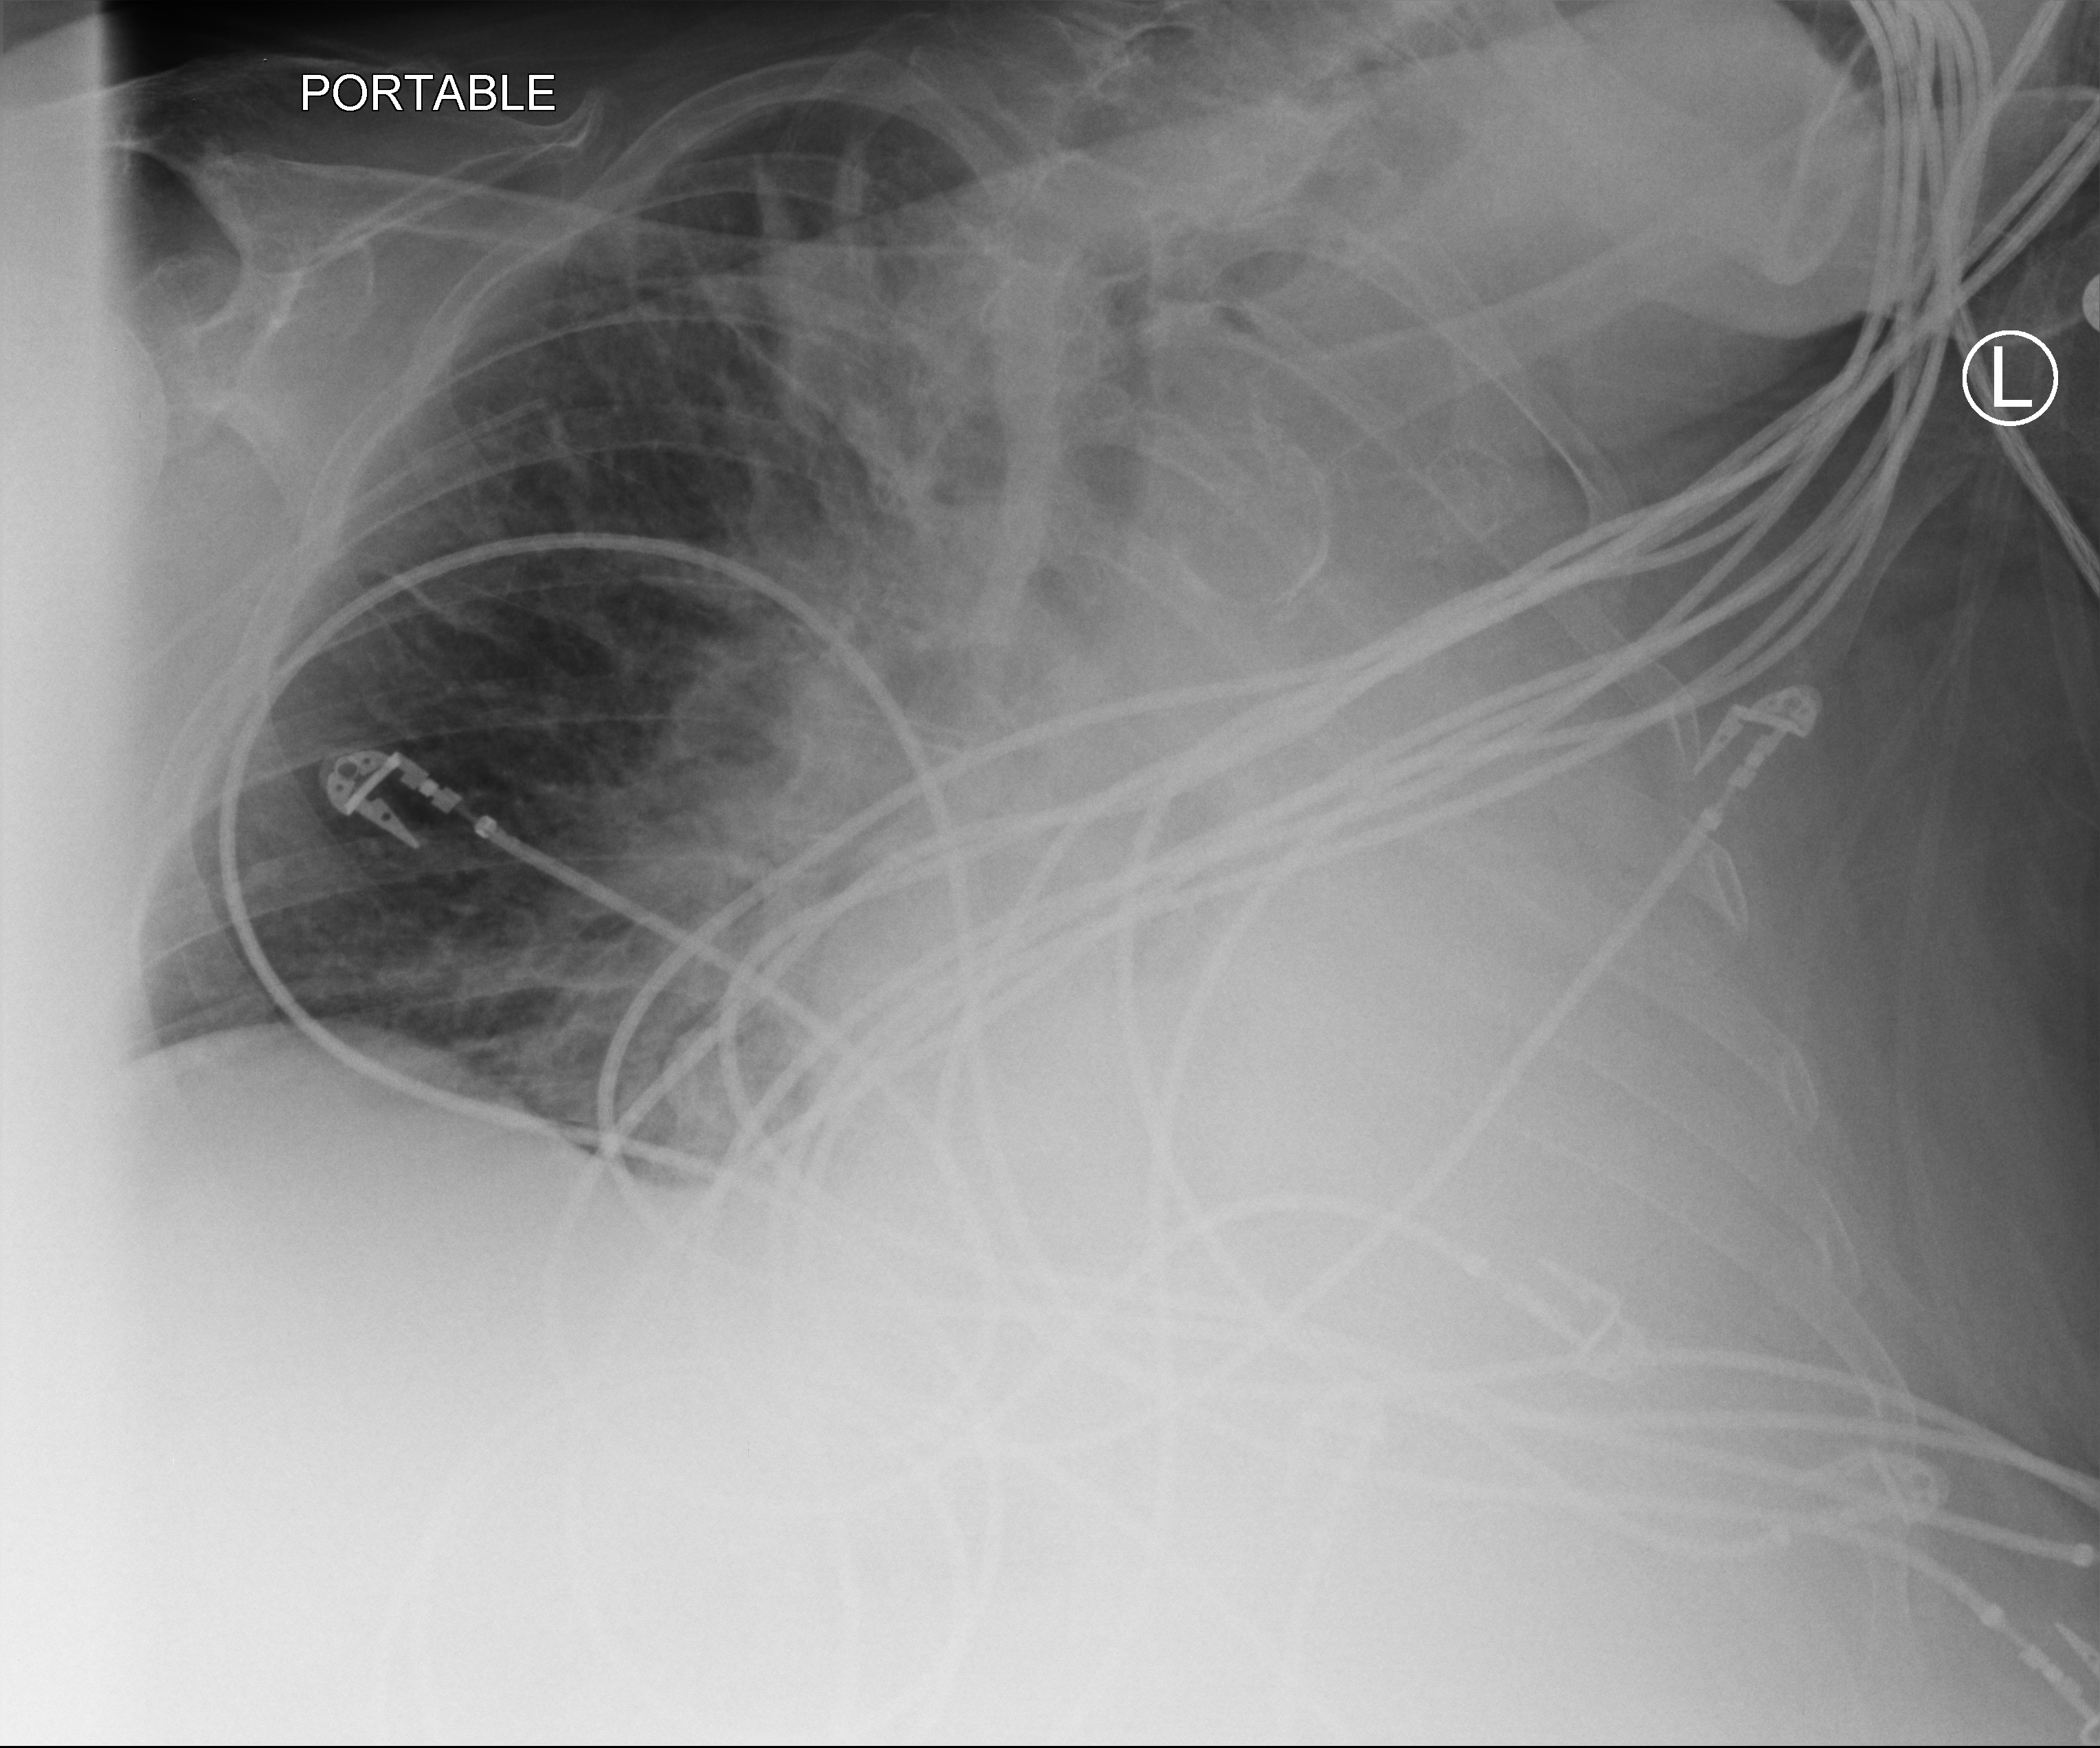
Chest X-ray (portable). Patient hospitalised with COVID-19; female, aged 75–90 years.
Hospital-stay facts (about this admission, not read from this image; timing relative to this image not recorded): length of hospital stay: 5 days; admitted to intensive care during this hospital stay: yes.